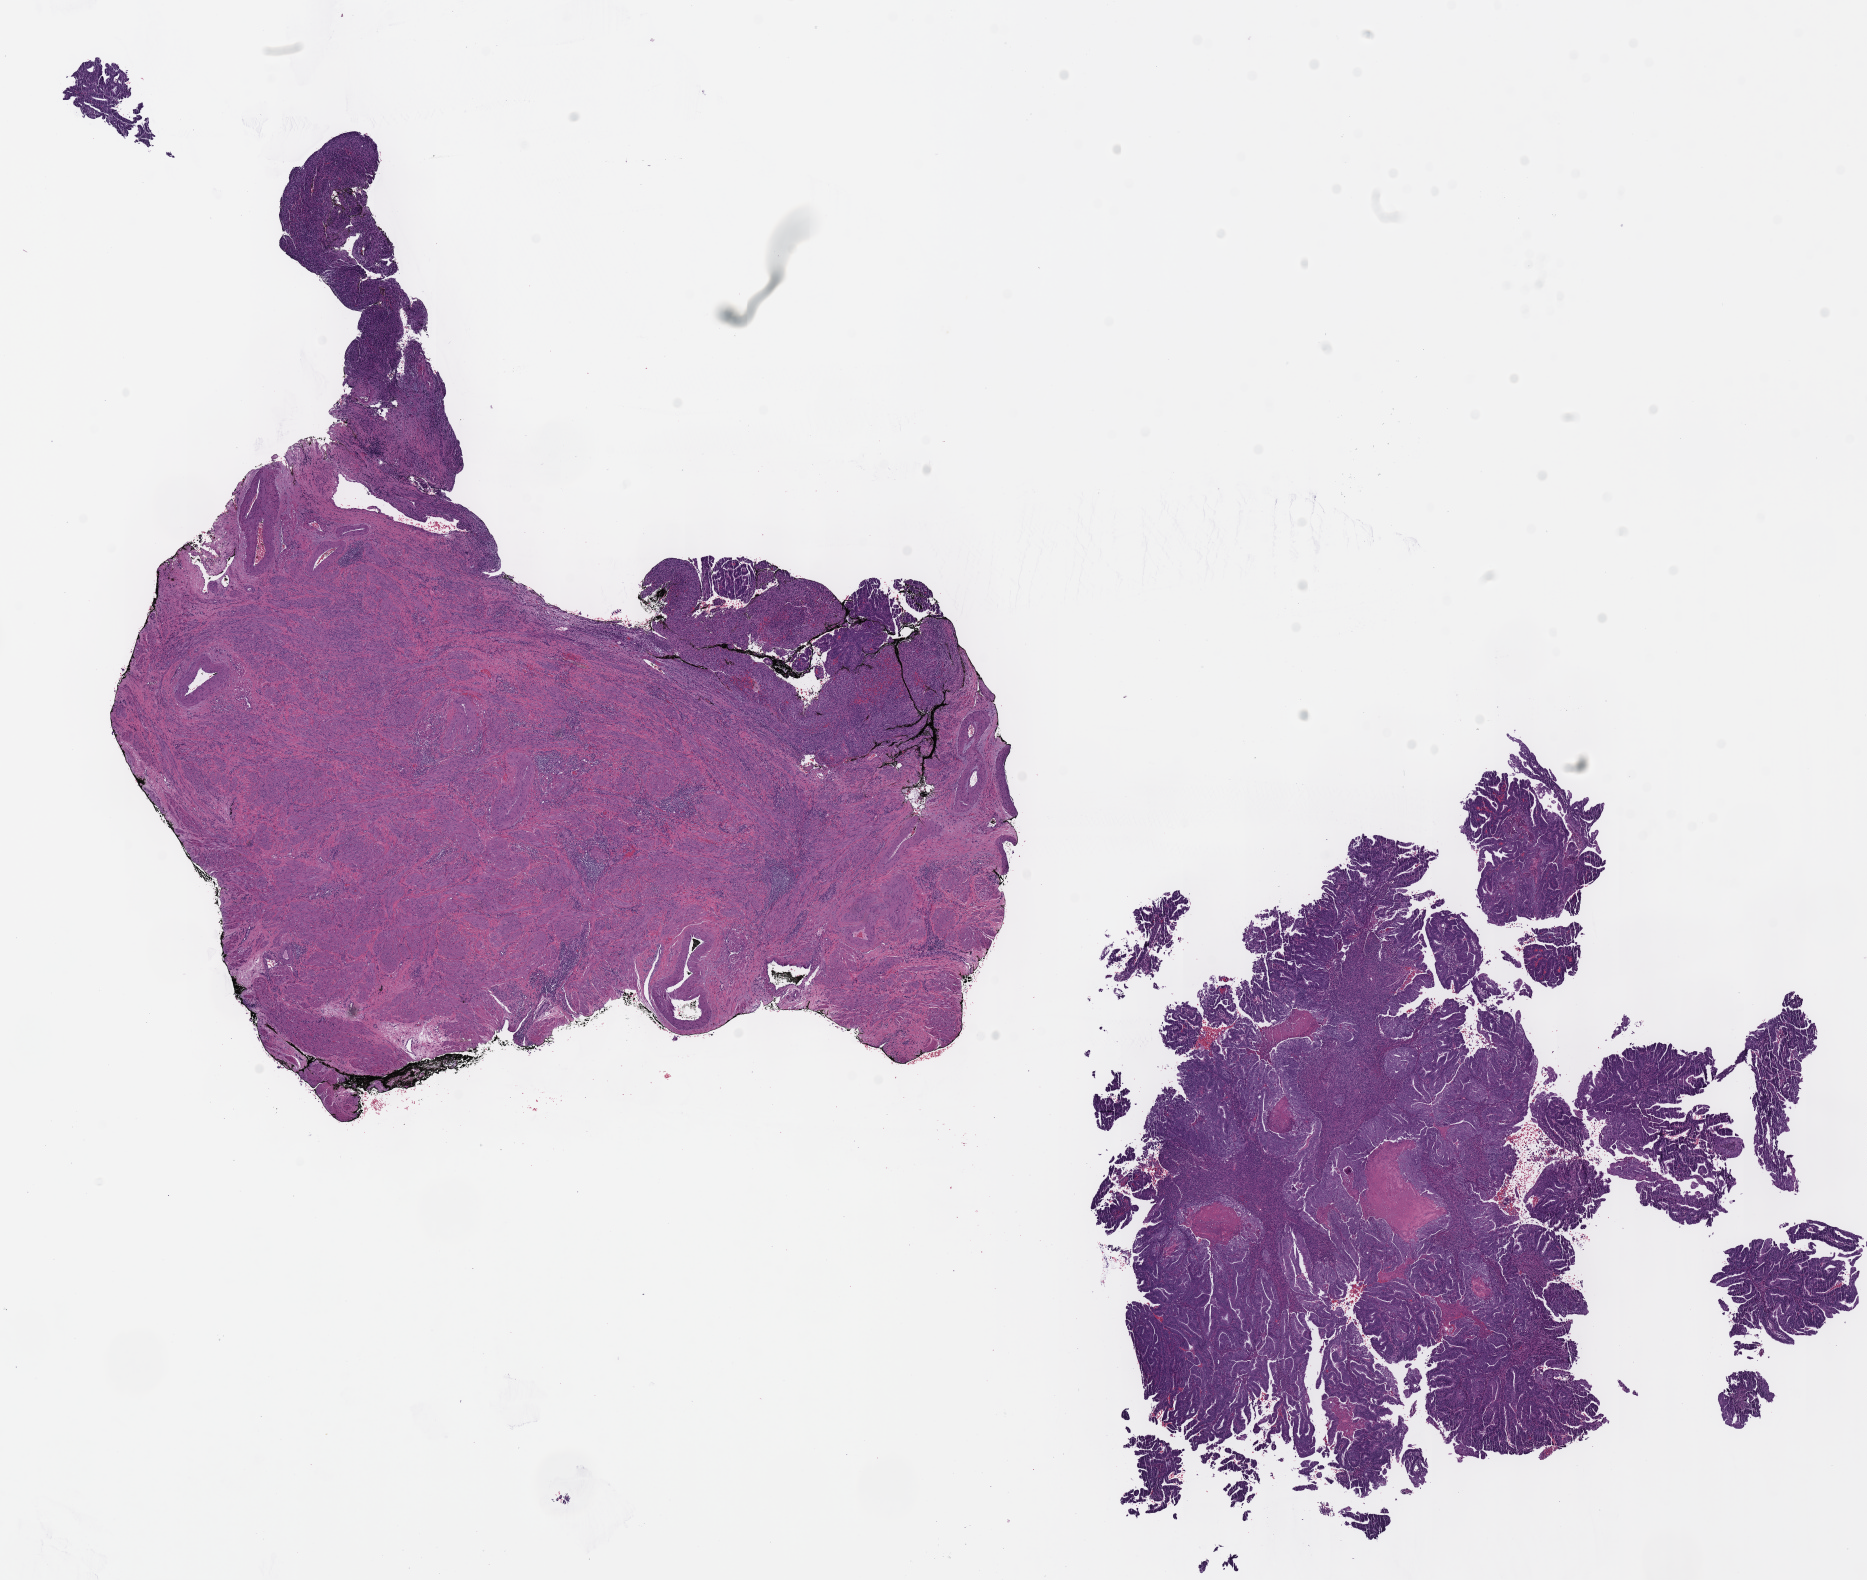
Digitized H&E-stained tissue section (whole slide), low-resolution overview of the scanned area, about 14.7 x 12.4 mm. Formalin-fixed paraffin-embedded (FFPE) diagnostic section. Sample: primary tumour, uterus. Female patient; age at initial diagnosis 46 years. Histologic grade: G3 (poorly differentiated).
- FIGO stage: IA
- diagnosis: Endometrioid adenocarcinoma, NOS (endometrium)
- lymph nodes positive (case pathology): 0 of 12 examined